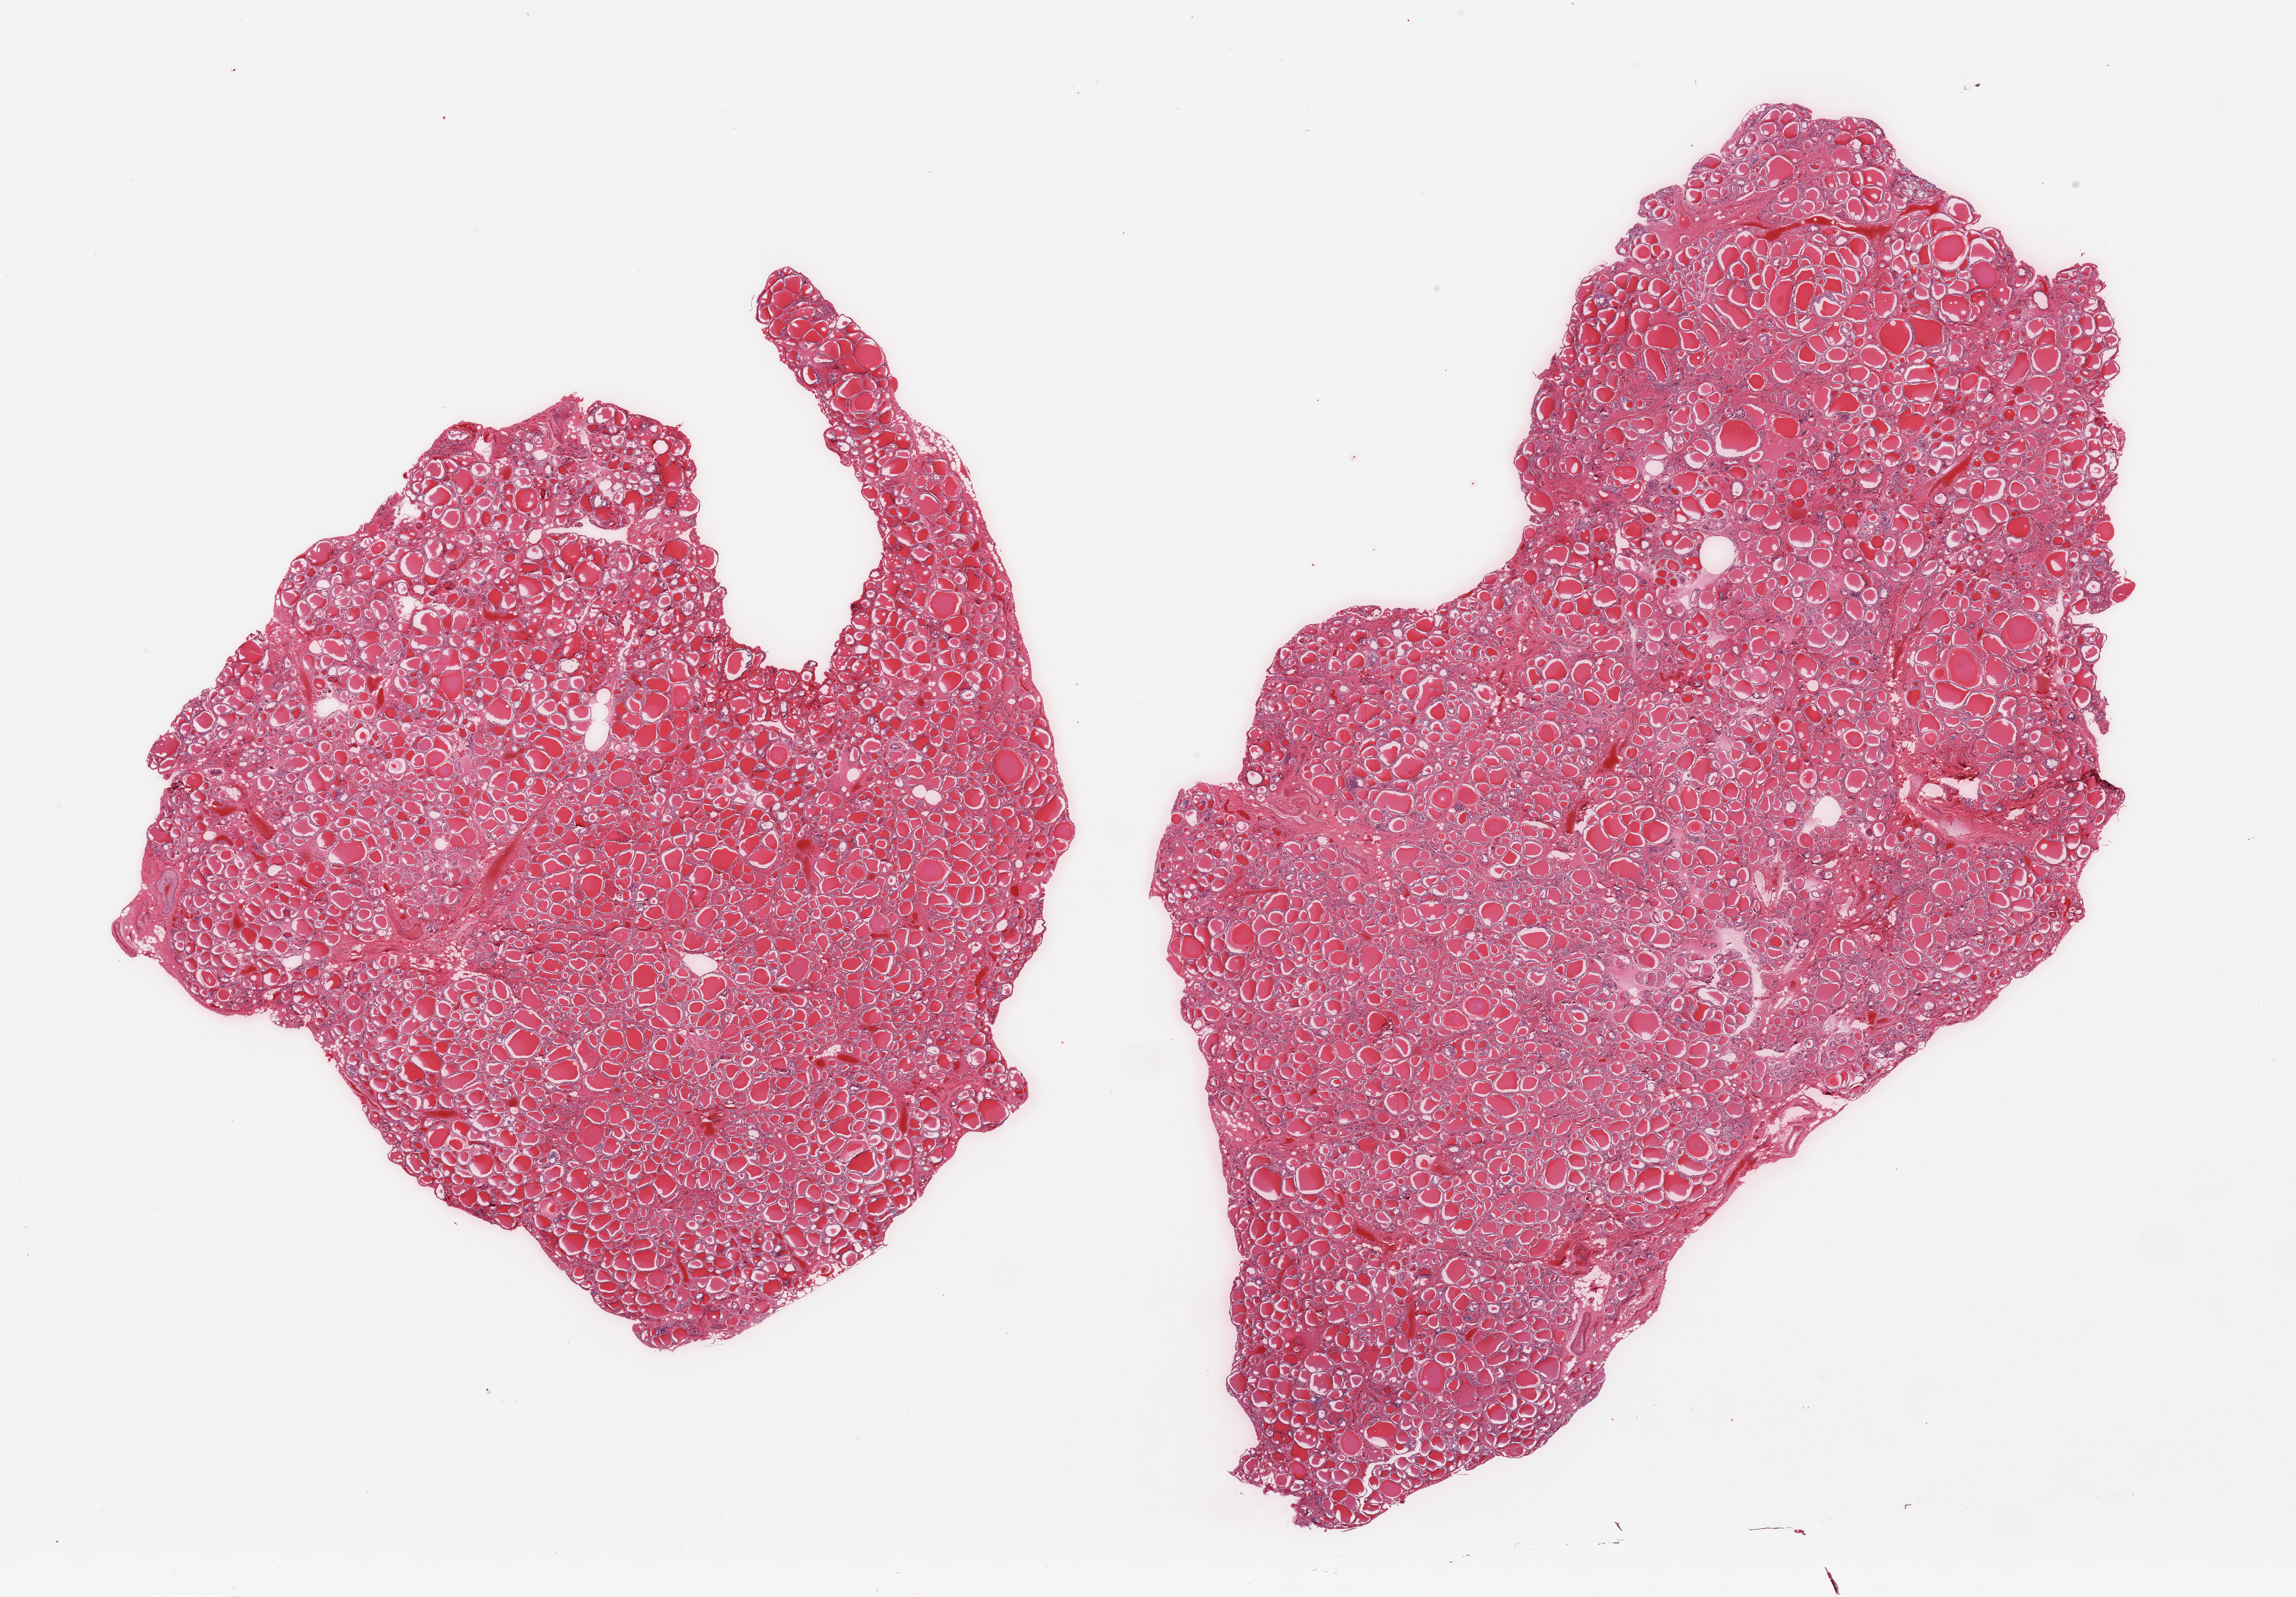
Hematoxylin and eosin (H&E) whole-slide image — whole scanned area (about 31.5 x 21.9 mm, from a 20x scan) shown as a low-resolution overview. PAXgene-fixed paraffin-embedded (PFPE) section. Section of thyroid (target tissue). Donor tissue sample. Donor sex: male.
* pathologist's review note for this sample: 2 pieces